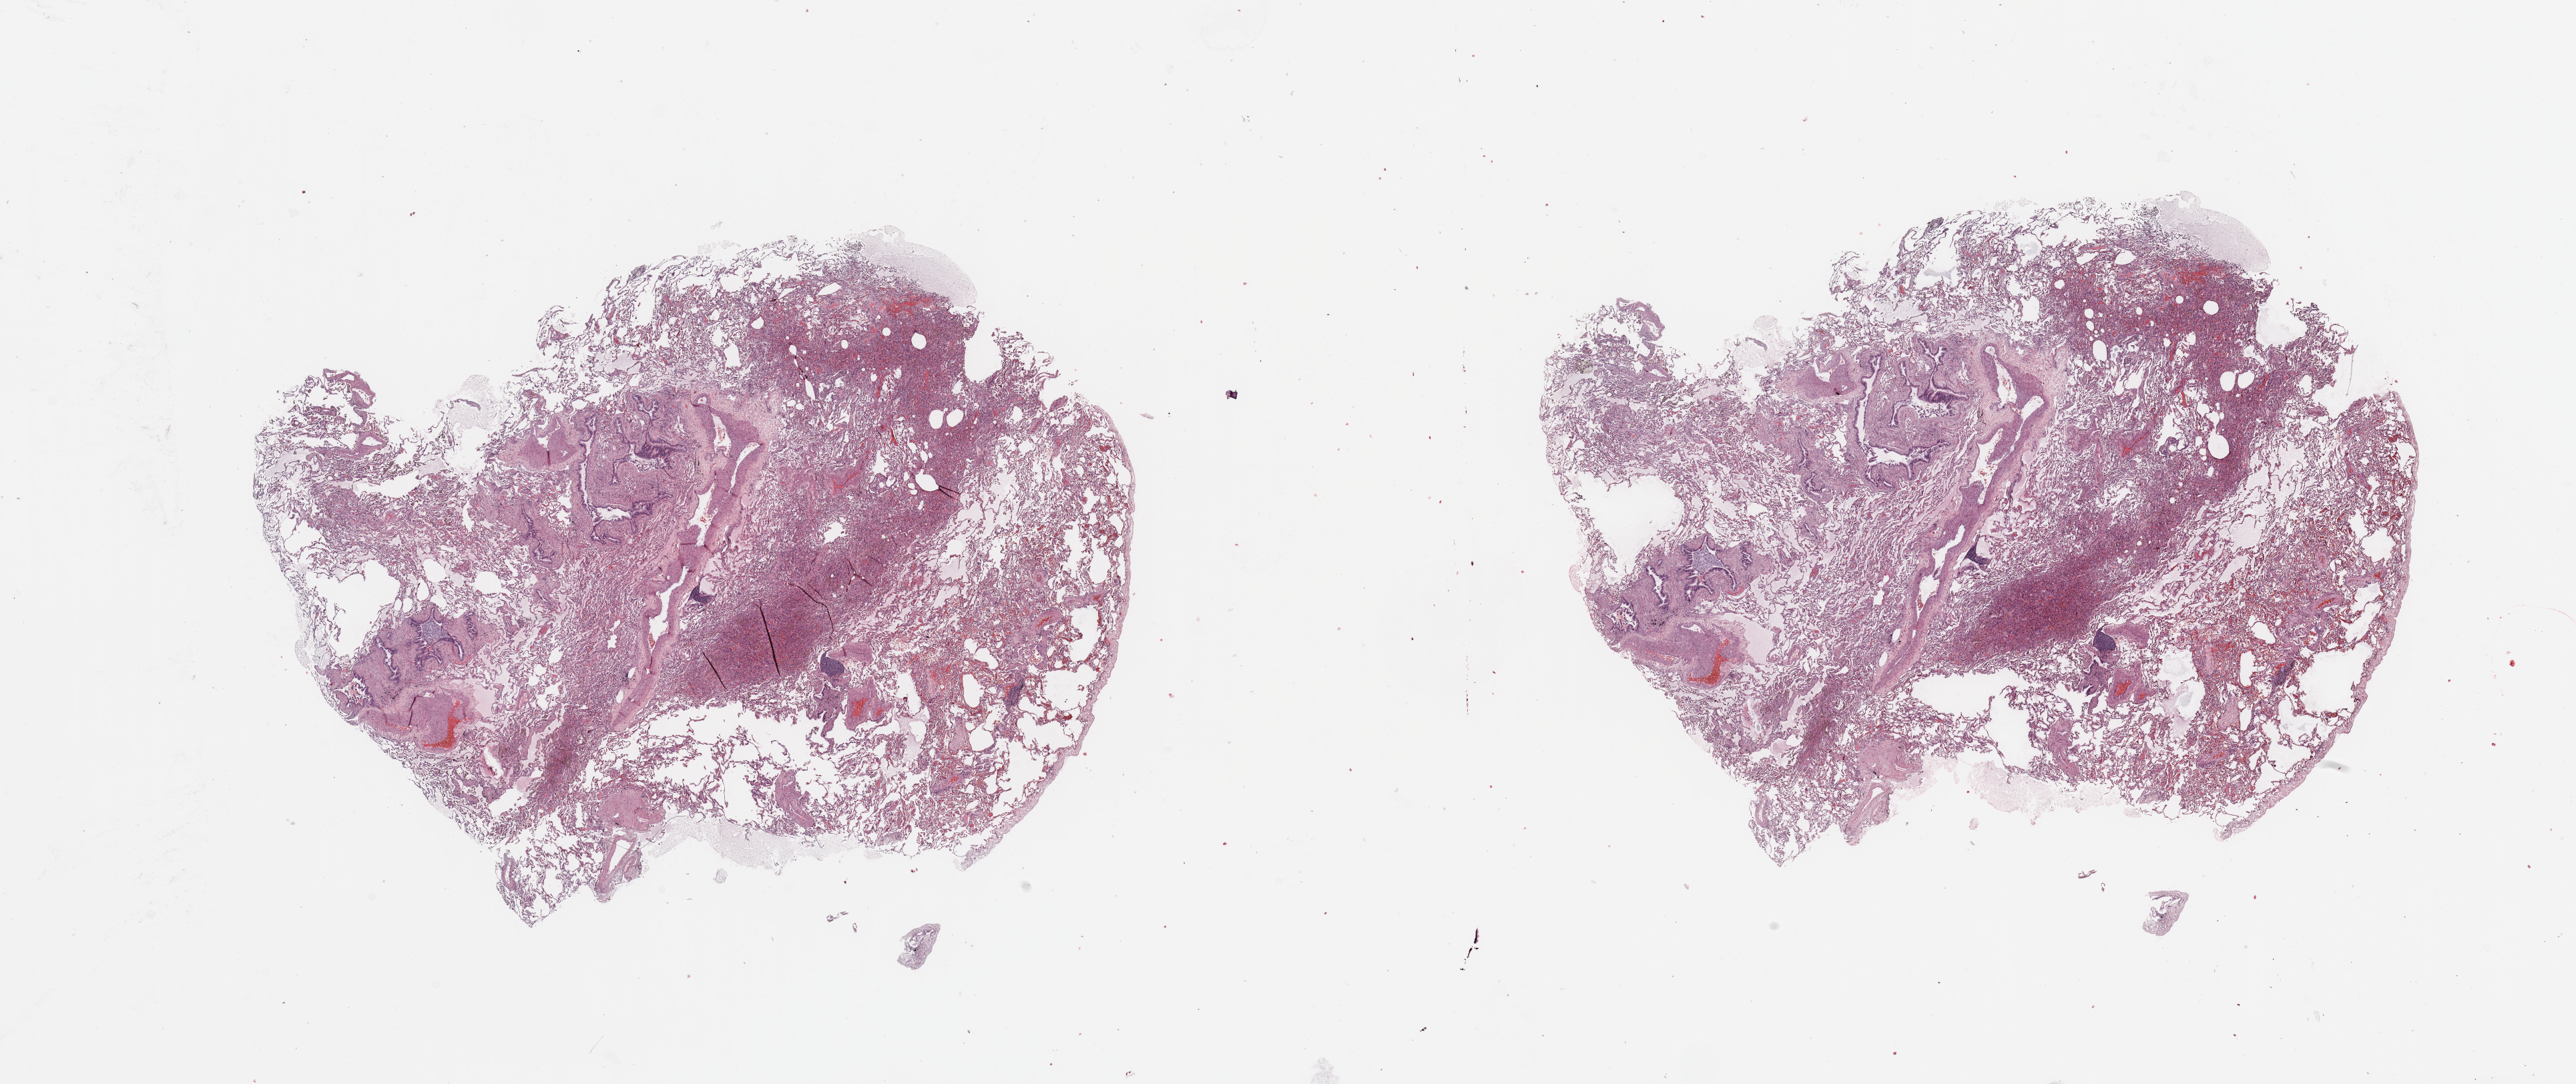
Whole-slide histology image, H&E — whole scanned area (about 30.5 x 12.8 mm, slide scanned at 20x) shown as a low-resolution overview; lung, normal (non-tumour) tissue. Patient: male, age 64 years.
- this section: normal (non-tumour) tissue from the same patient
- patient diagnosis: Adenocarcinoma, NOS